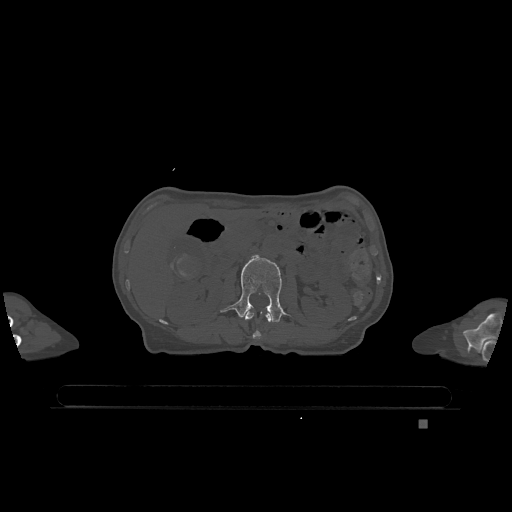
CT including the spine, one axial slice; slice 428 of 1317 in the series (ordered by position); bone window (W 1800 / L 400 HU); 0.5 mm slice thickness; 512 × 512 image matrix, field of view 500 × 500 mm. Patient: female, 74 years. From the clinical record (not read from this slice): primary cancer: lung; vertebrae with lytic lesions (as recorded): T1, T4, T5, T6, L4, L5.
Annotated regions visible in this slice (semi-automatic segmentation, software-assisted and operator-edited):
- L1 vertebra: bounding box (x1, y1, x2, y2) in pixels: (244, 311, 272, 339)
- L2 vertebra: (221, 255, 286, 323)